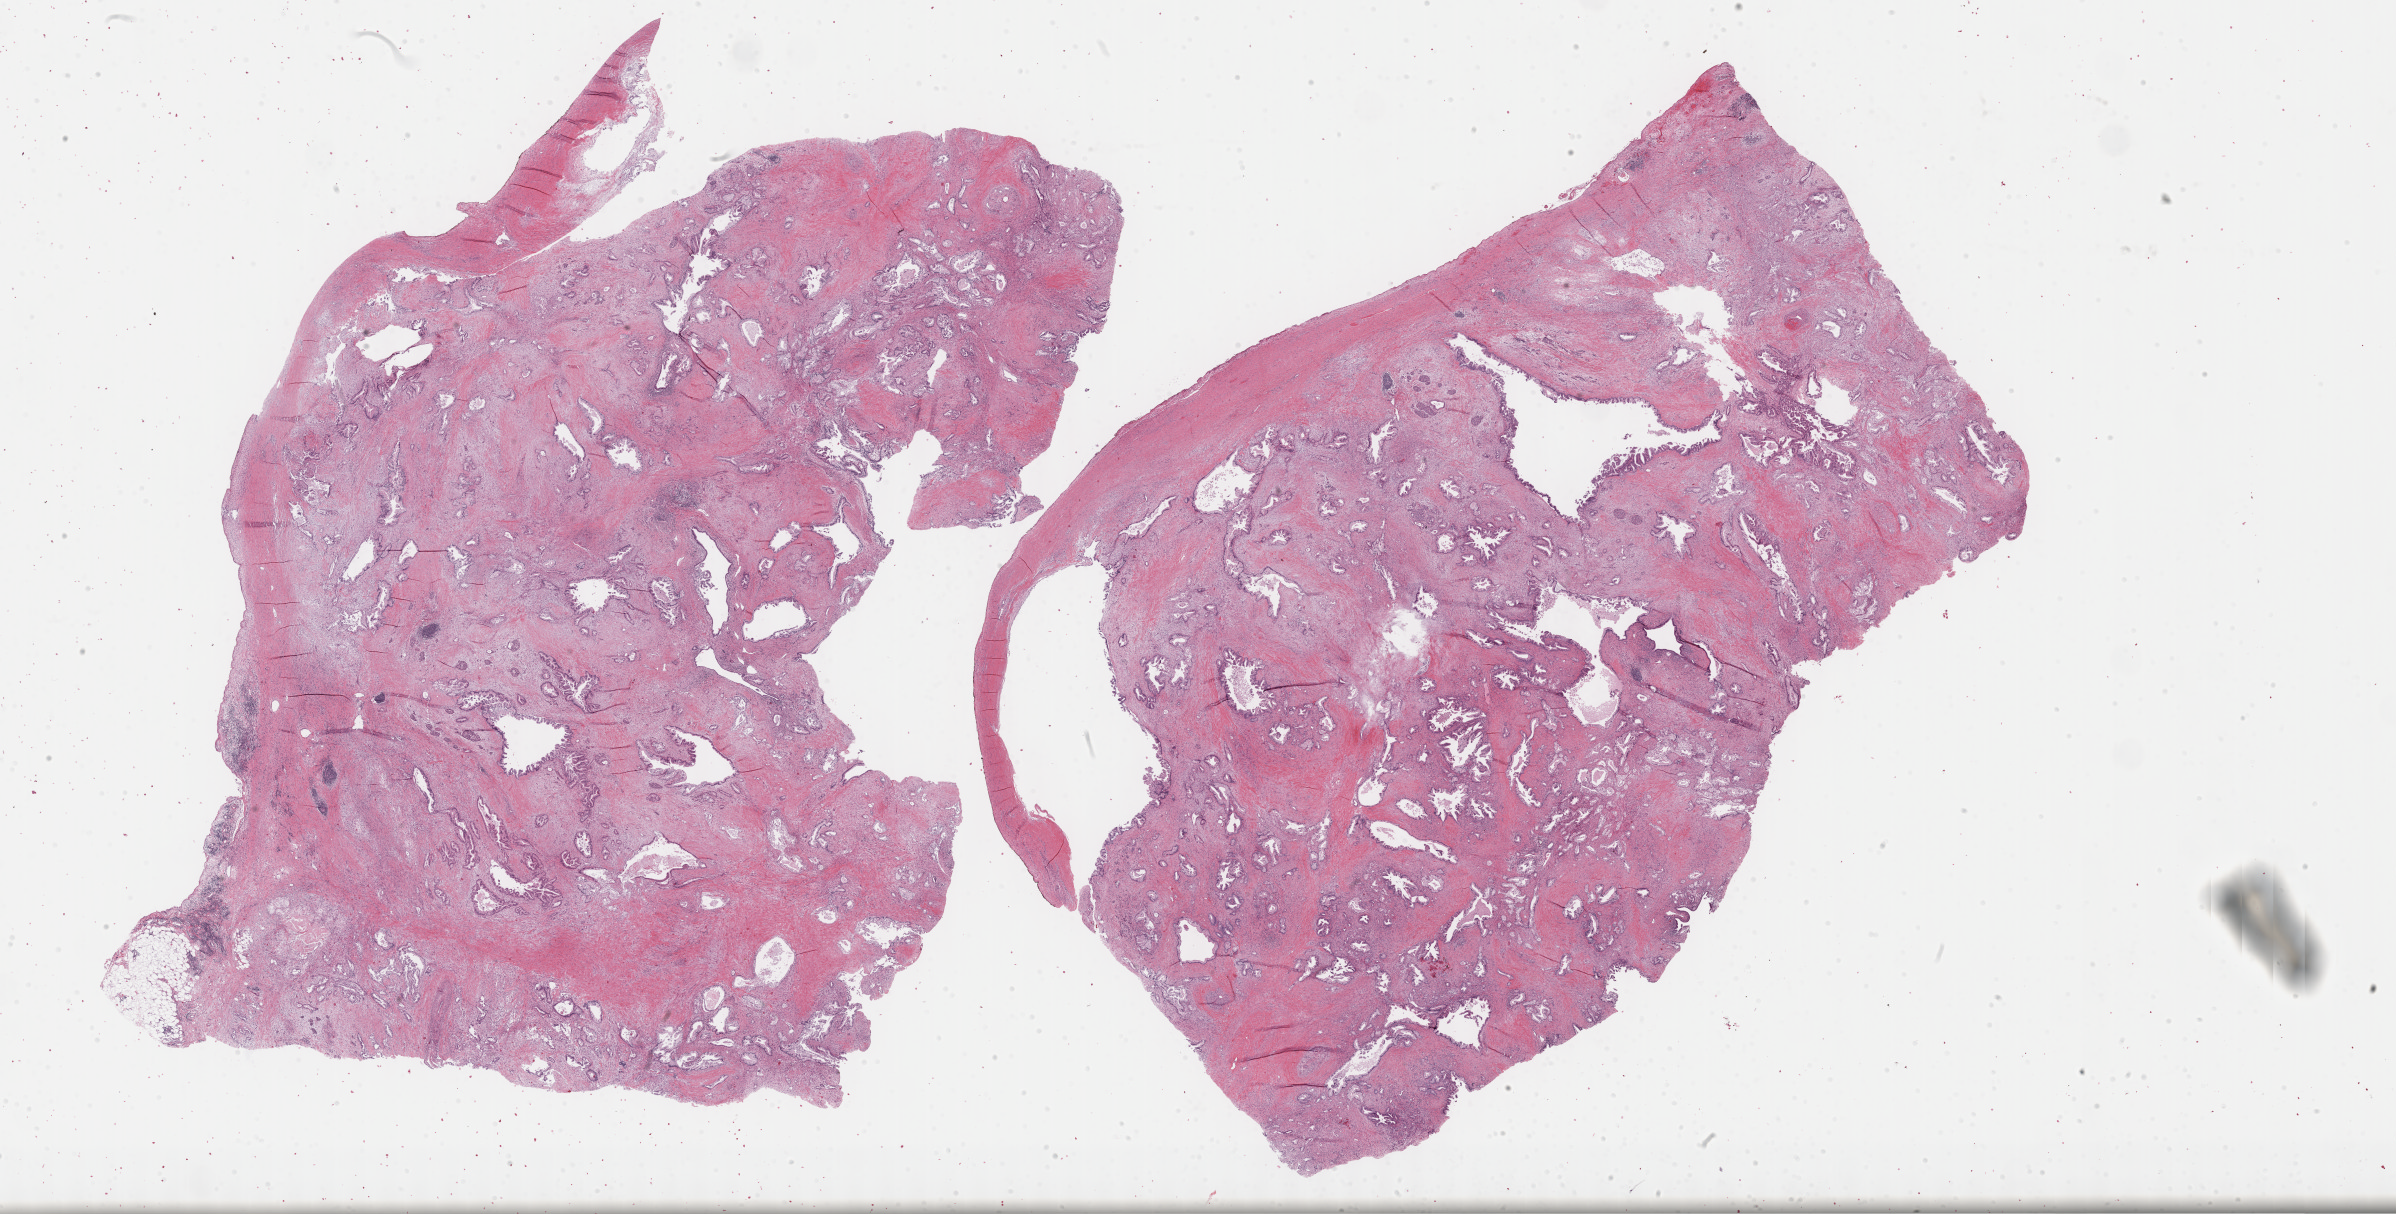
Whole-slide histology image, H&E-stained, shown as a low-resolution overview of the whole scanned area (about 38.8 x 19.6 mm, acquisition: 40x scan); formalin-fixed paraffin-embedded (FFPE) diagnostic section; sample: primary tumour, pancreas. Male, age 73 years at initial diagnosis. Histologic grade: G2 (moderately differentiated).
* AJCC pathologic stage: IIA (7th edition)
* diagnosis: Infiltrating duct carcinoma, NOS (body of pancreas)
* lymph nodes positive (case pathology): 0 of 24 examined